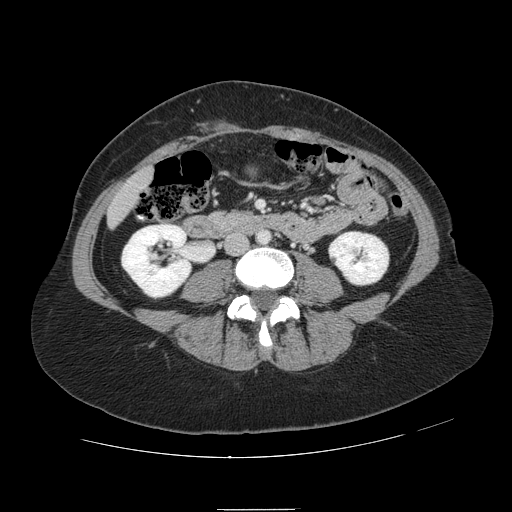
Contrast-enhanced abdominal CT, one axial slice. Slice 5 of 121 in the series (ordered by position). 120 kVp. Intravenous contrast given. Soft-tissue window (W 400 / L 40 HU). 2.5 mm slice thickness. 512 × 512 image matrix, field of view 400 × 400 mm. Female patient, age 52 years. Case-level facts recorded for this patient, not image findings: diagnosis: colorectal cancer liver metastases, imaged before liver resection; multiple liver metastases: yes; largest metastasis: 6.3 cm; disease in both lobes: no.
Outlined on this slice (outlined manually by an expert reader):
- liver: bounding box [x1, y1, x2, y2] px = [110, 170, 152, 224]